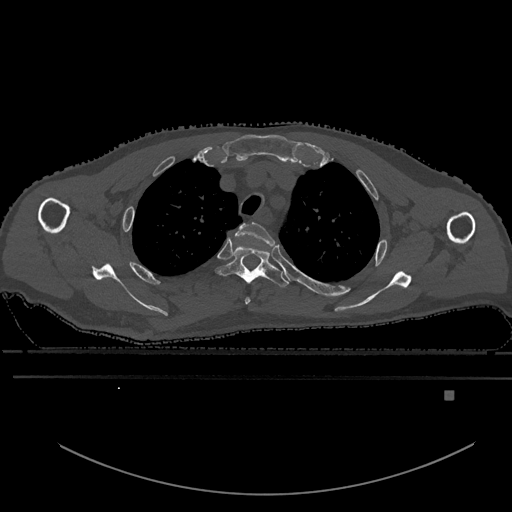
CT including the spine, one axial slice. Bone window (W 1800 / L 400 HU). 0.5 mm slice thickness. 512 × 512 image matrix, field of view 456 × 456 mm. Patient: male, 82 years. From the clinical record (not read from this slice): primary cancer: prostate.
Outlined on this slice (semi-automatically segmented with operator editing):
- T2 vertebra: bounding box <235,221,275,305> (left, top, right, bottom; pixels)
- T3 vertebra: <216,246,289,287>